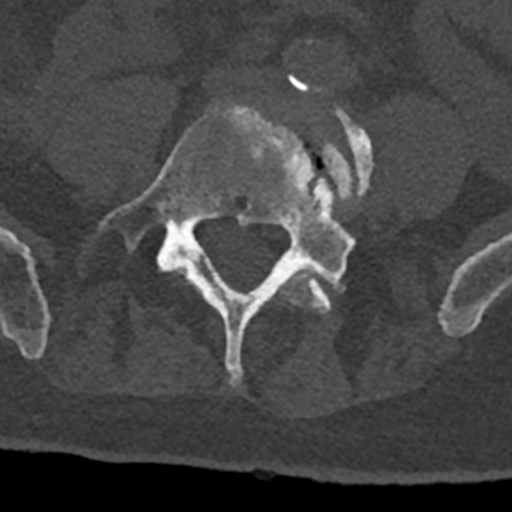
CT including the spine, one axial slice; position 213 of 797 along the scan axis; reconstruction kernel Br40s/3; bone window (W 1800 / L 400 HU); 0.5 mm slice thickness; 512 × 512 image matrix. Male patient, age 74 years. Case-level facts recorded for this patient, not image findings: primary cancer: renal; vertebrae with lytic lesions (as recorded): T10, L1, L2, L3, L4, L5.
Annotated regions visible in this slice (semi-automatically segmented with operator editing):
- L4 vertebra: bounding box [x1, y1, x2, y2] px = [177, 85, 374, 314]
- L5 vertebra: [100, 102, 355, 386]